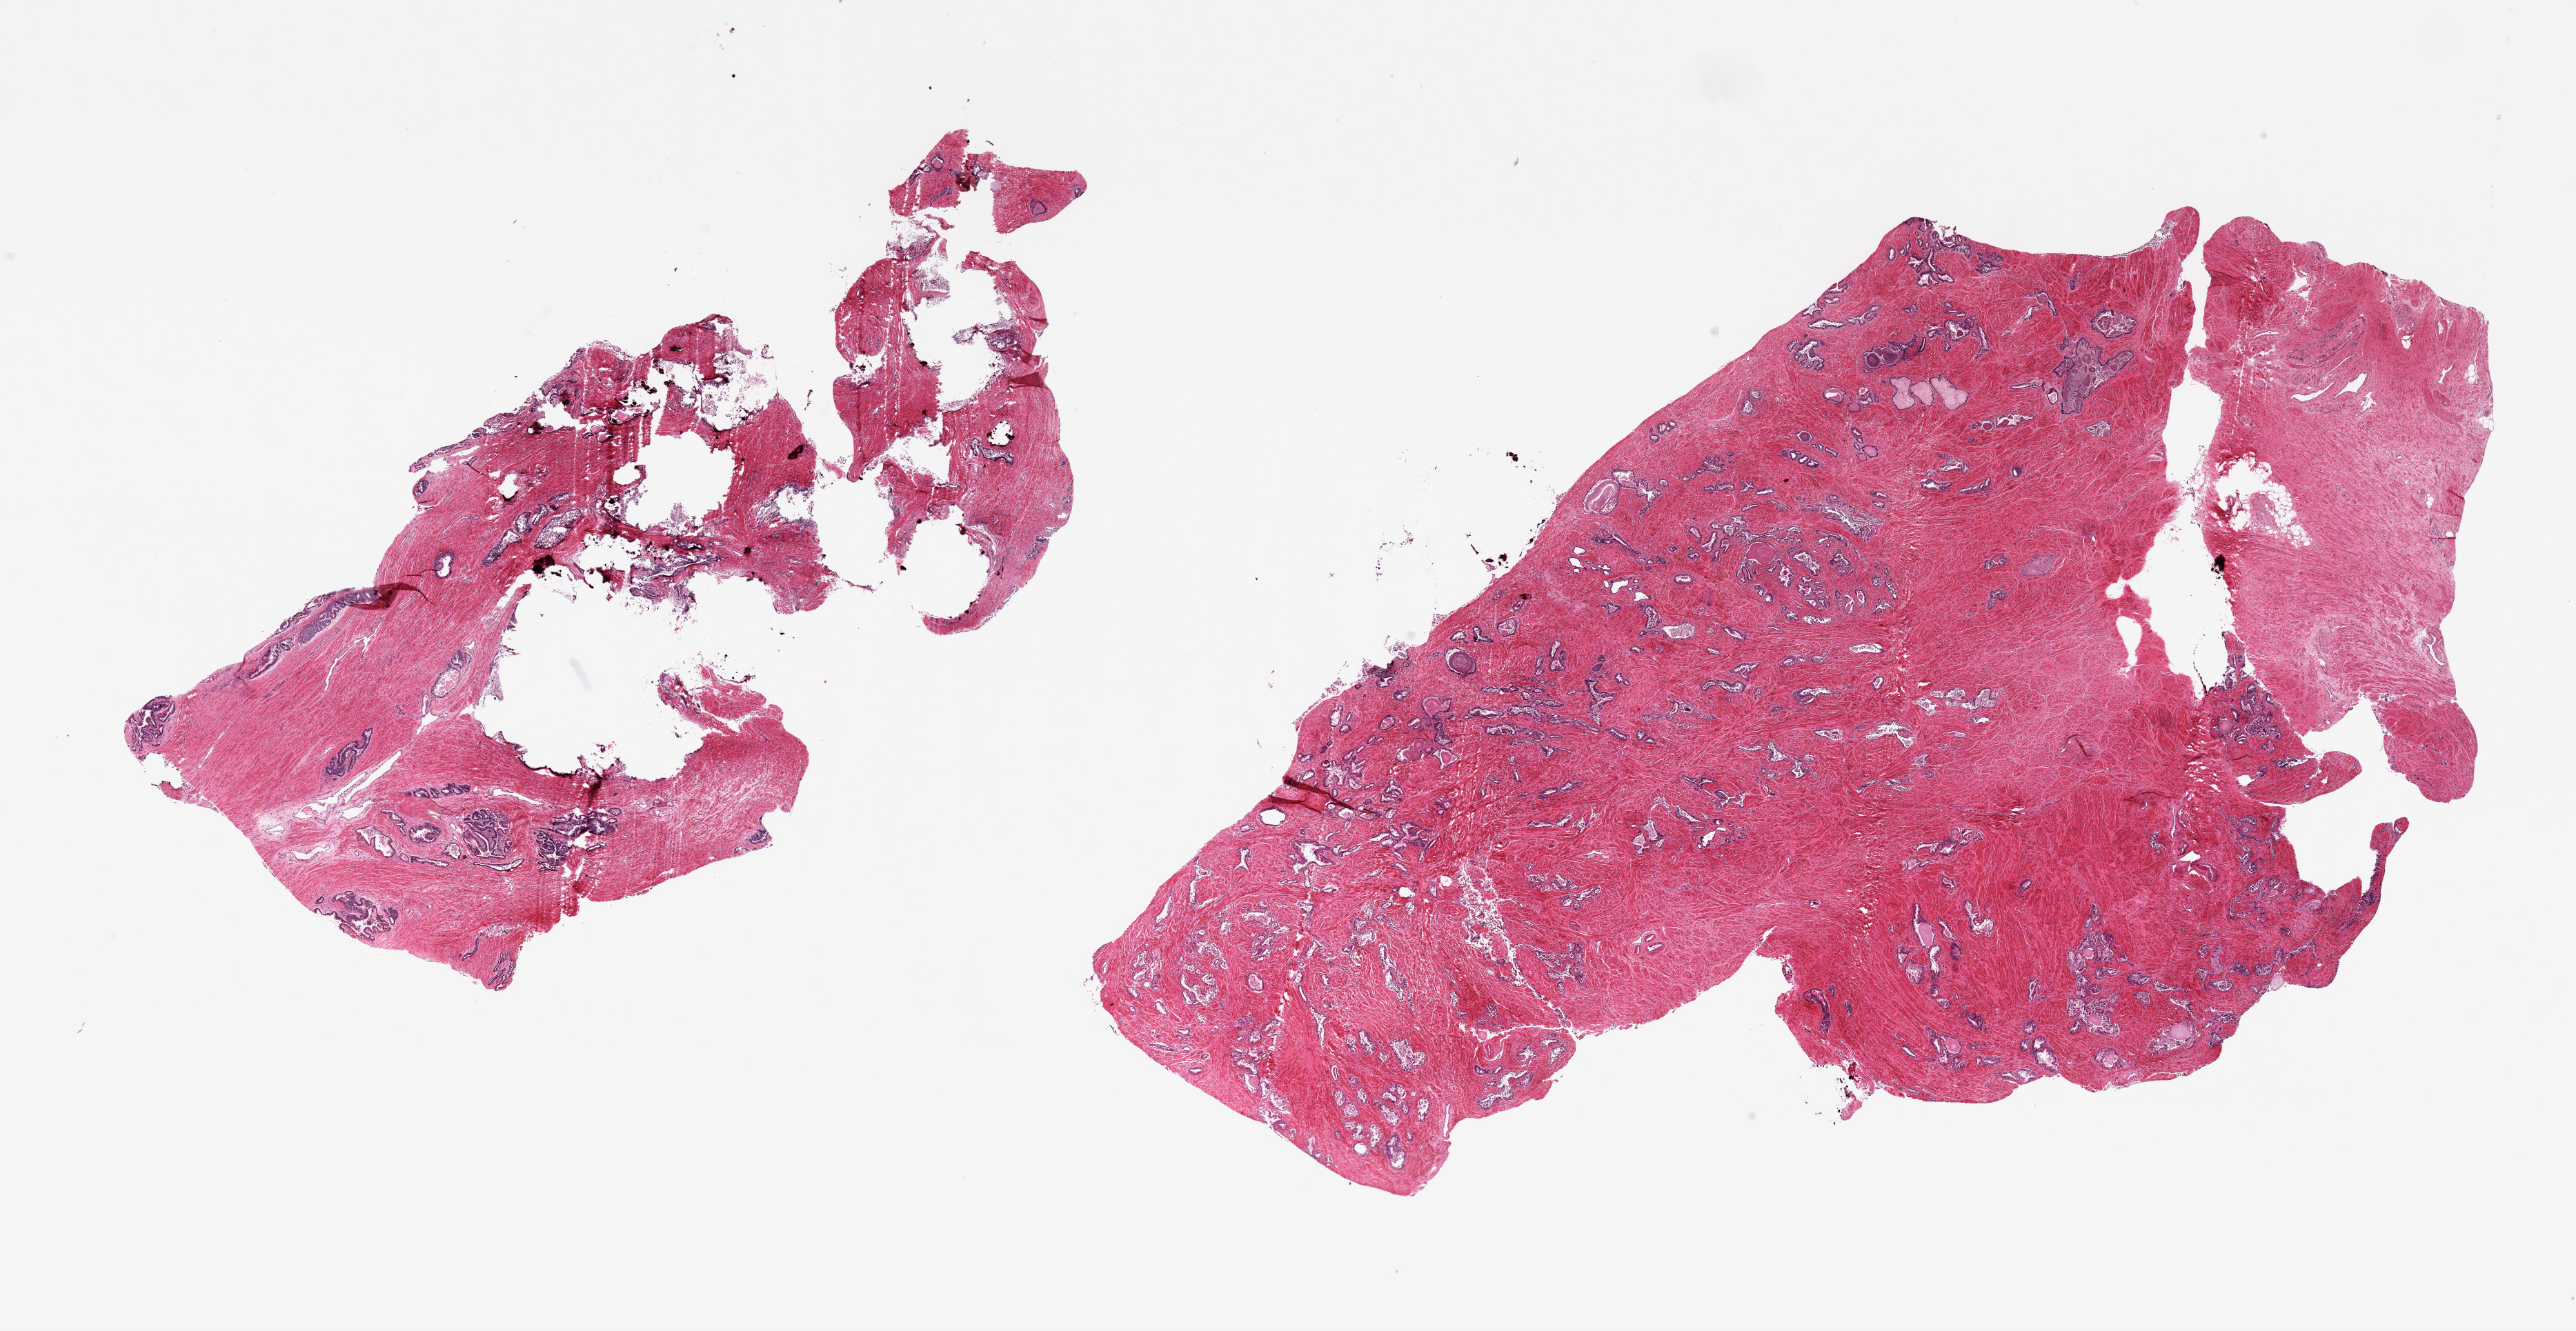
Haematoxylin and eosin whole-slide image, a low-resolution overview of the entire scanned area, about 29.5 x 15.3 mm. PAXgene-fixed paraffin-embedded (PFPE) section. Section of prostate (target tissue). Donor tissue sample. Donor: male.
Pathologist's review note for this sample: 2 pieces, glandular elements with moderate-advanced autolysis.